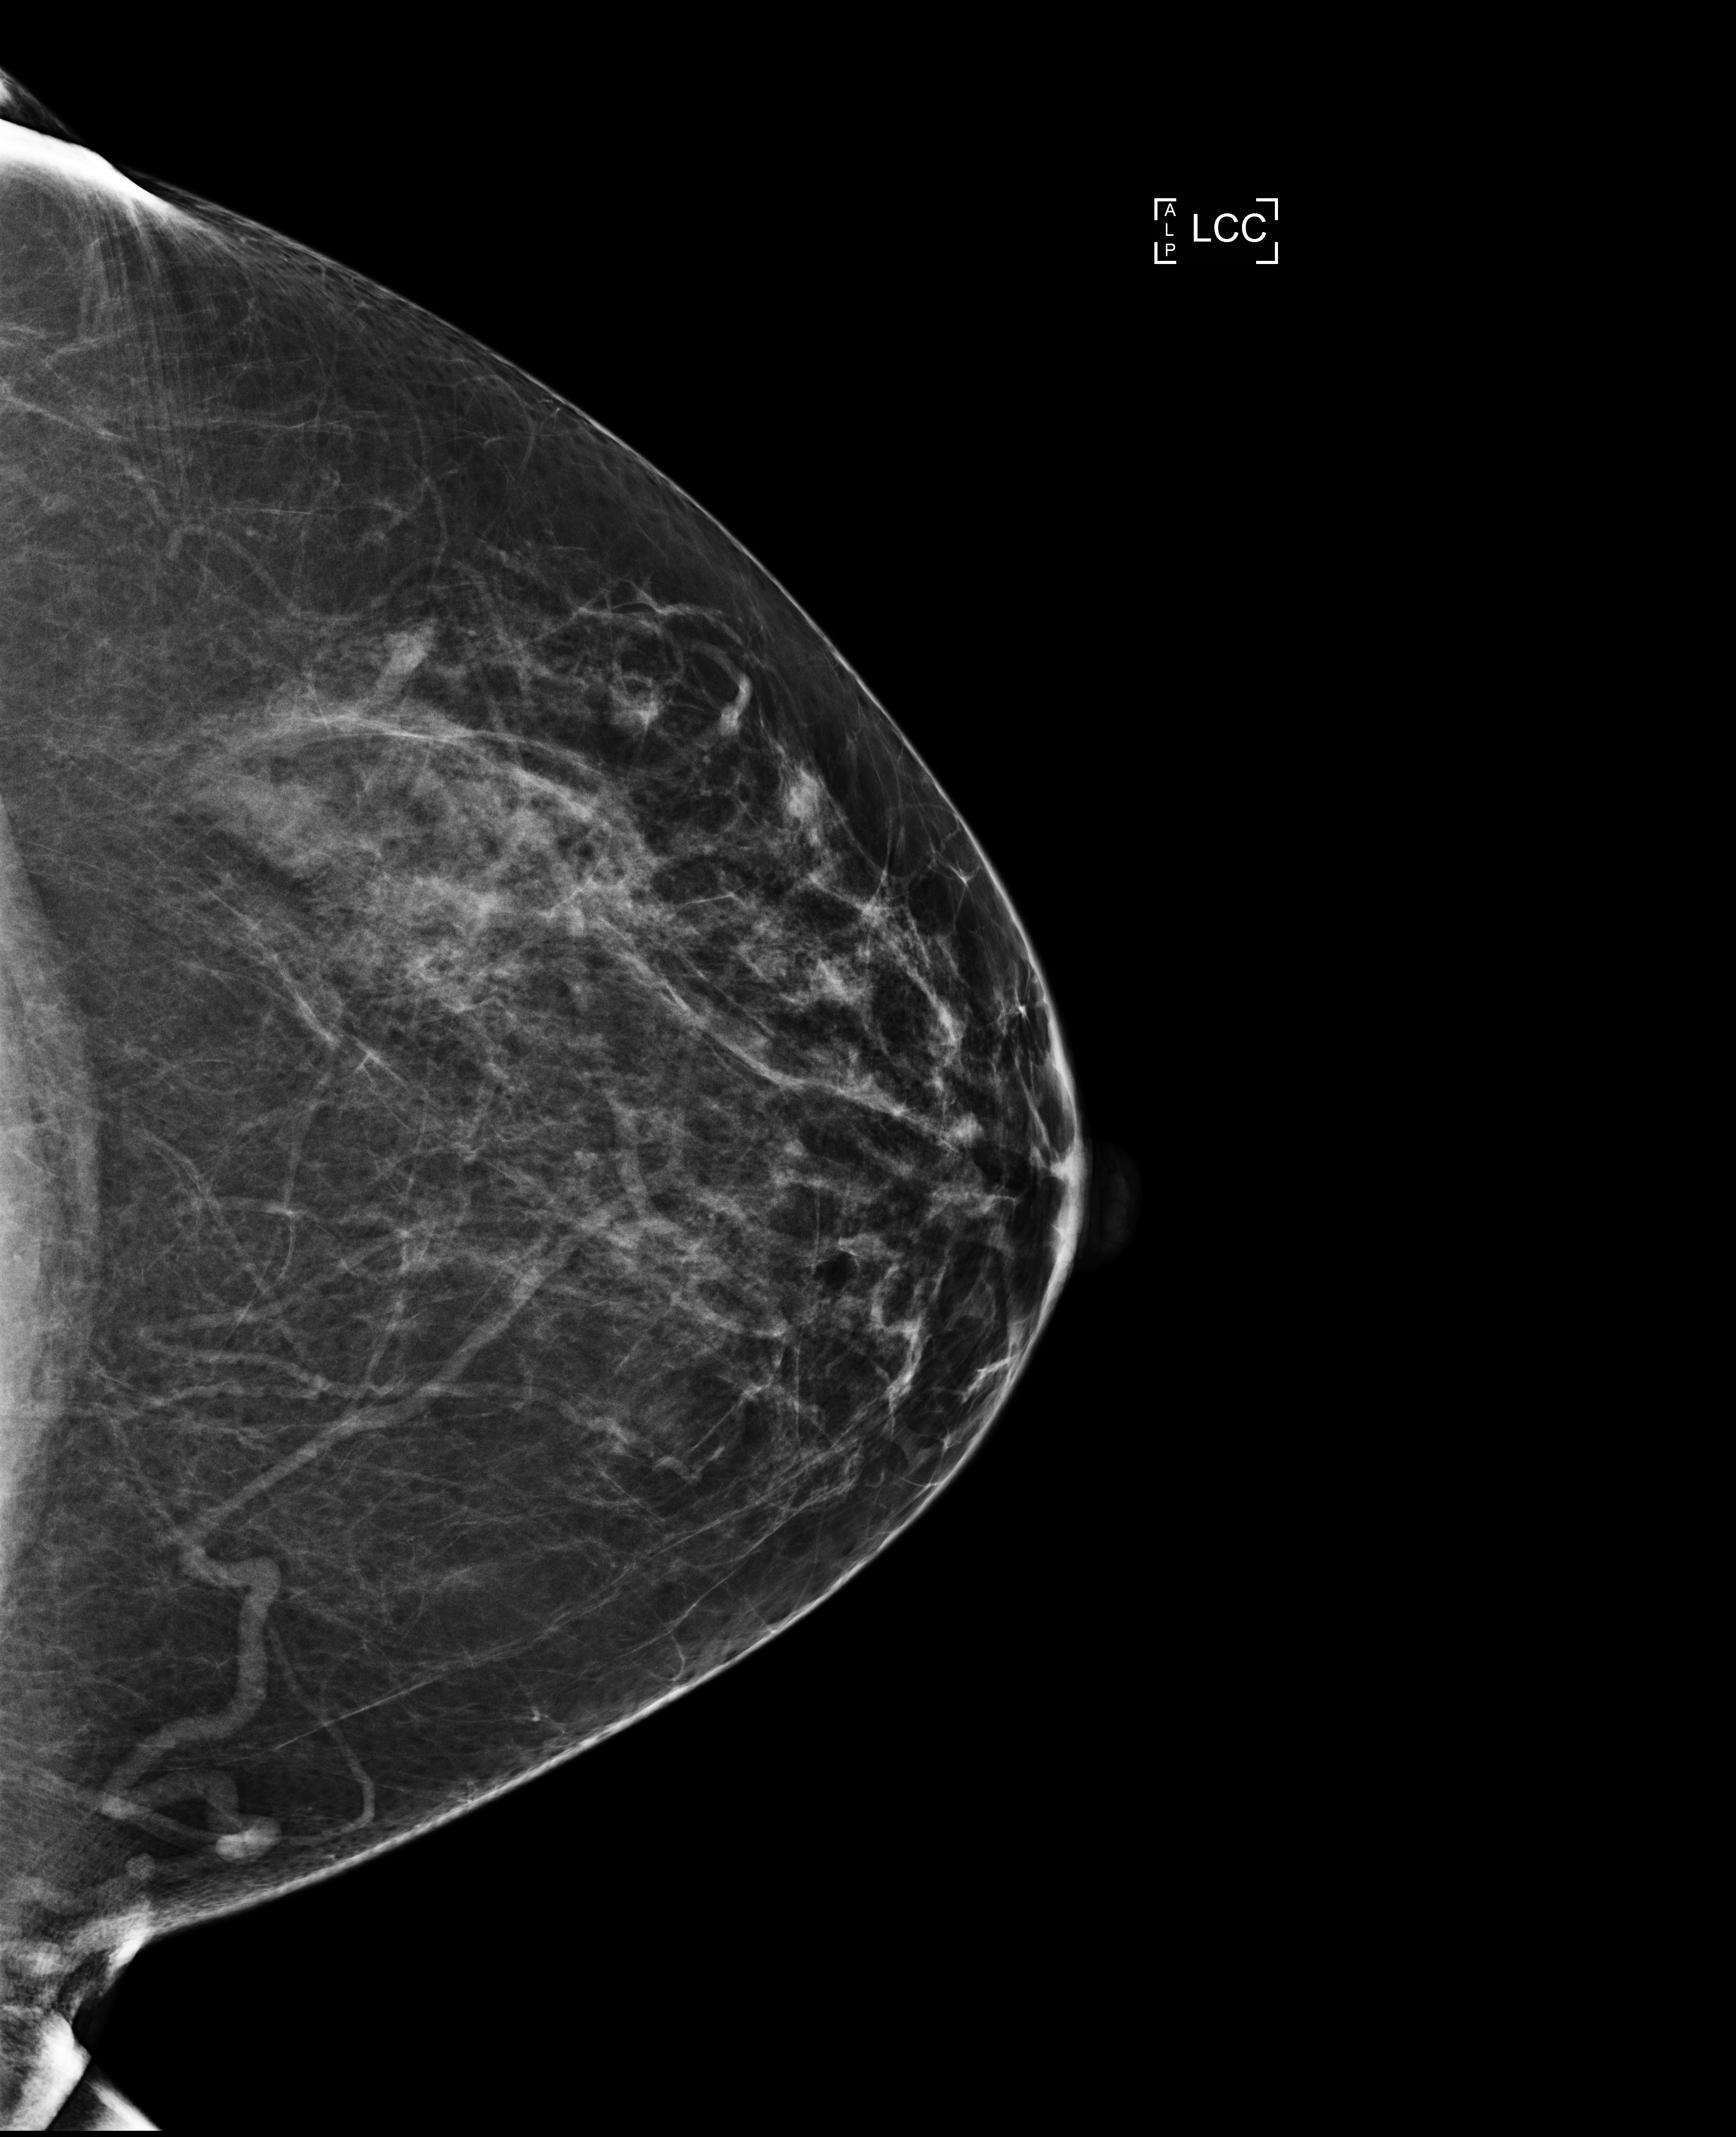
Digital mammogram (FFDM); left breast; CC view; screening examination; compressed breast thickness 80 mm; system: Selenia Dimensions. Patient aged 52 years (female).
Breast density at the screening exam (both breasts): heterogeneously dense (BI-RADS density category c). Final BI-RADS category for the screening round (tomosynthesis exam, both breasts): category 1. Recall: no recall after this screen.